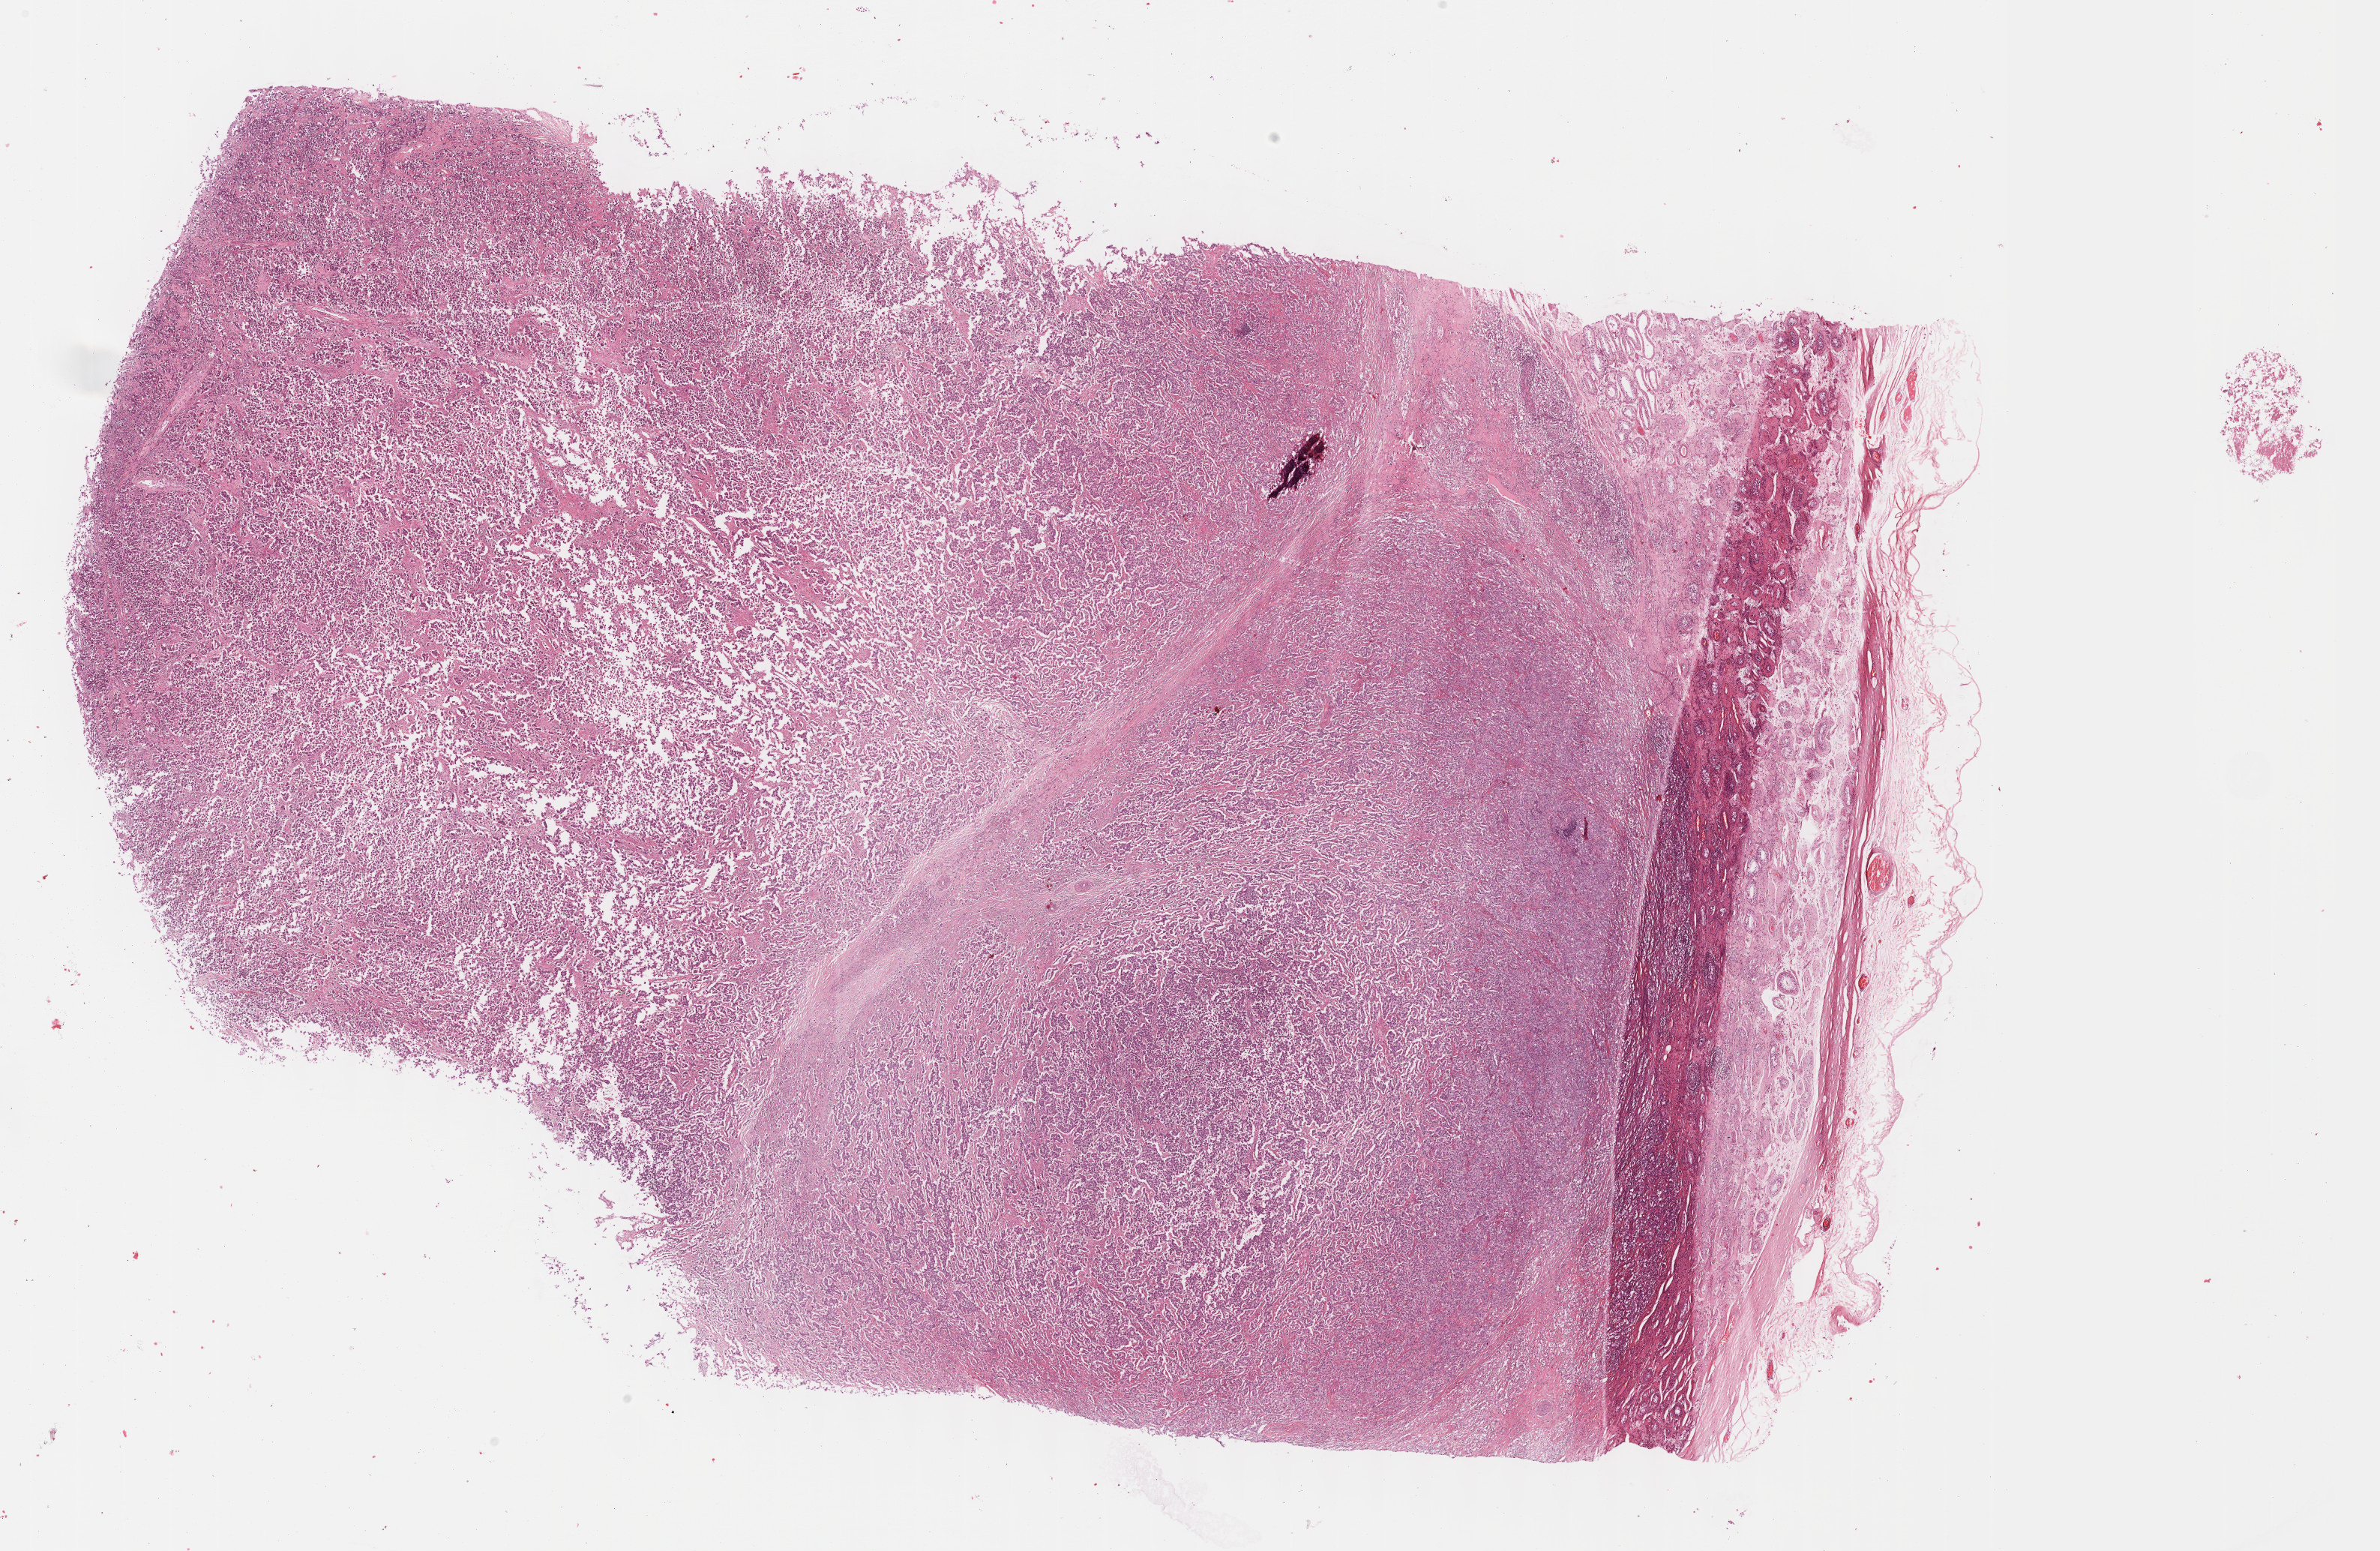
Digitized H&E-stained tissue section (whole slide) — low-resolution overview of the scanned area, about 25.7 x 16.7 mm (slide scanned at 40x); formalin-fixed paraffin-embedded (FFPE) diagnostic section; sample: primary tumour, testis. Male, age 35 years at initial diagnosis.
Pathologic diagnosis: Seminoma, NOS.